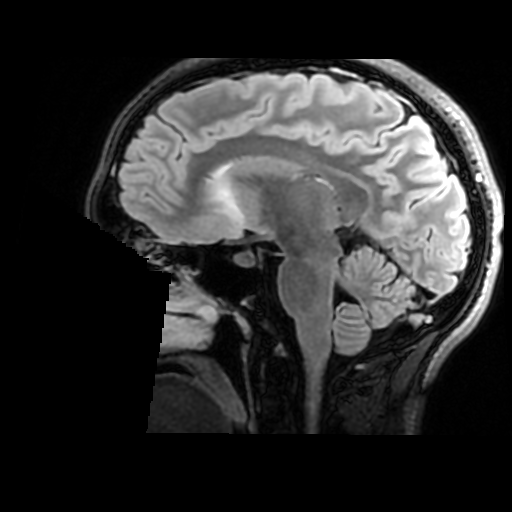
Brain MRI from a brain-tumour surgery series, one sagittal slice. Position 95 of 176 along the scan axis. T2 FLAIR. 1 mm slice thickness. 512 × 512 image matrix, field of view 240 × 240 mm. Case-level facts recorded for this patient, not image findings: histopathology: Astrocytoma; WHO grade: 2; IDH mutation: yes; tumour location: Right Insular.
Annotated regions visible in this slice (outlined manually by an expert reader):
- tumour: bounding box <204,179,241,218> (left, top, right, bottom; pixels)